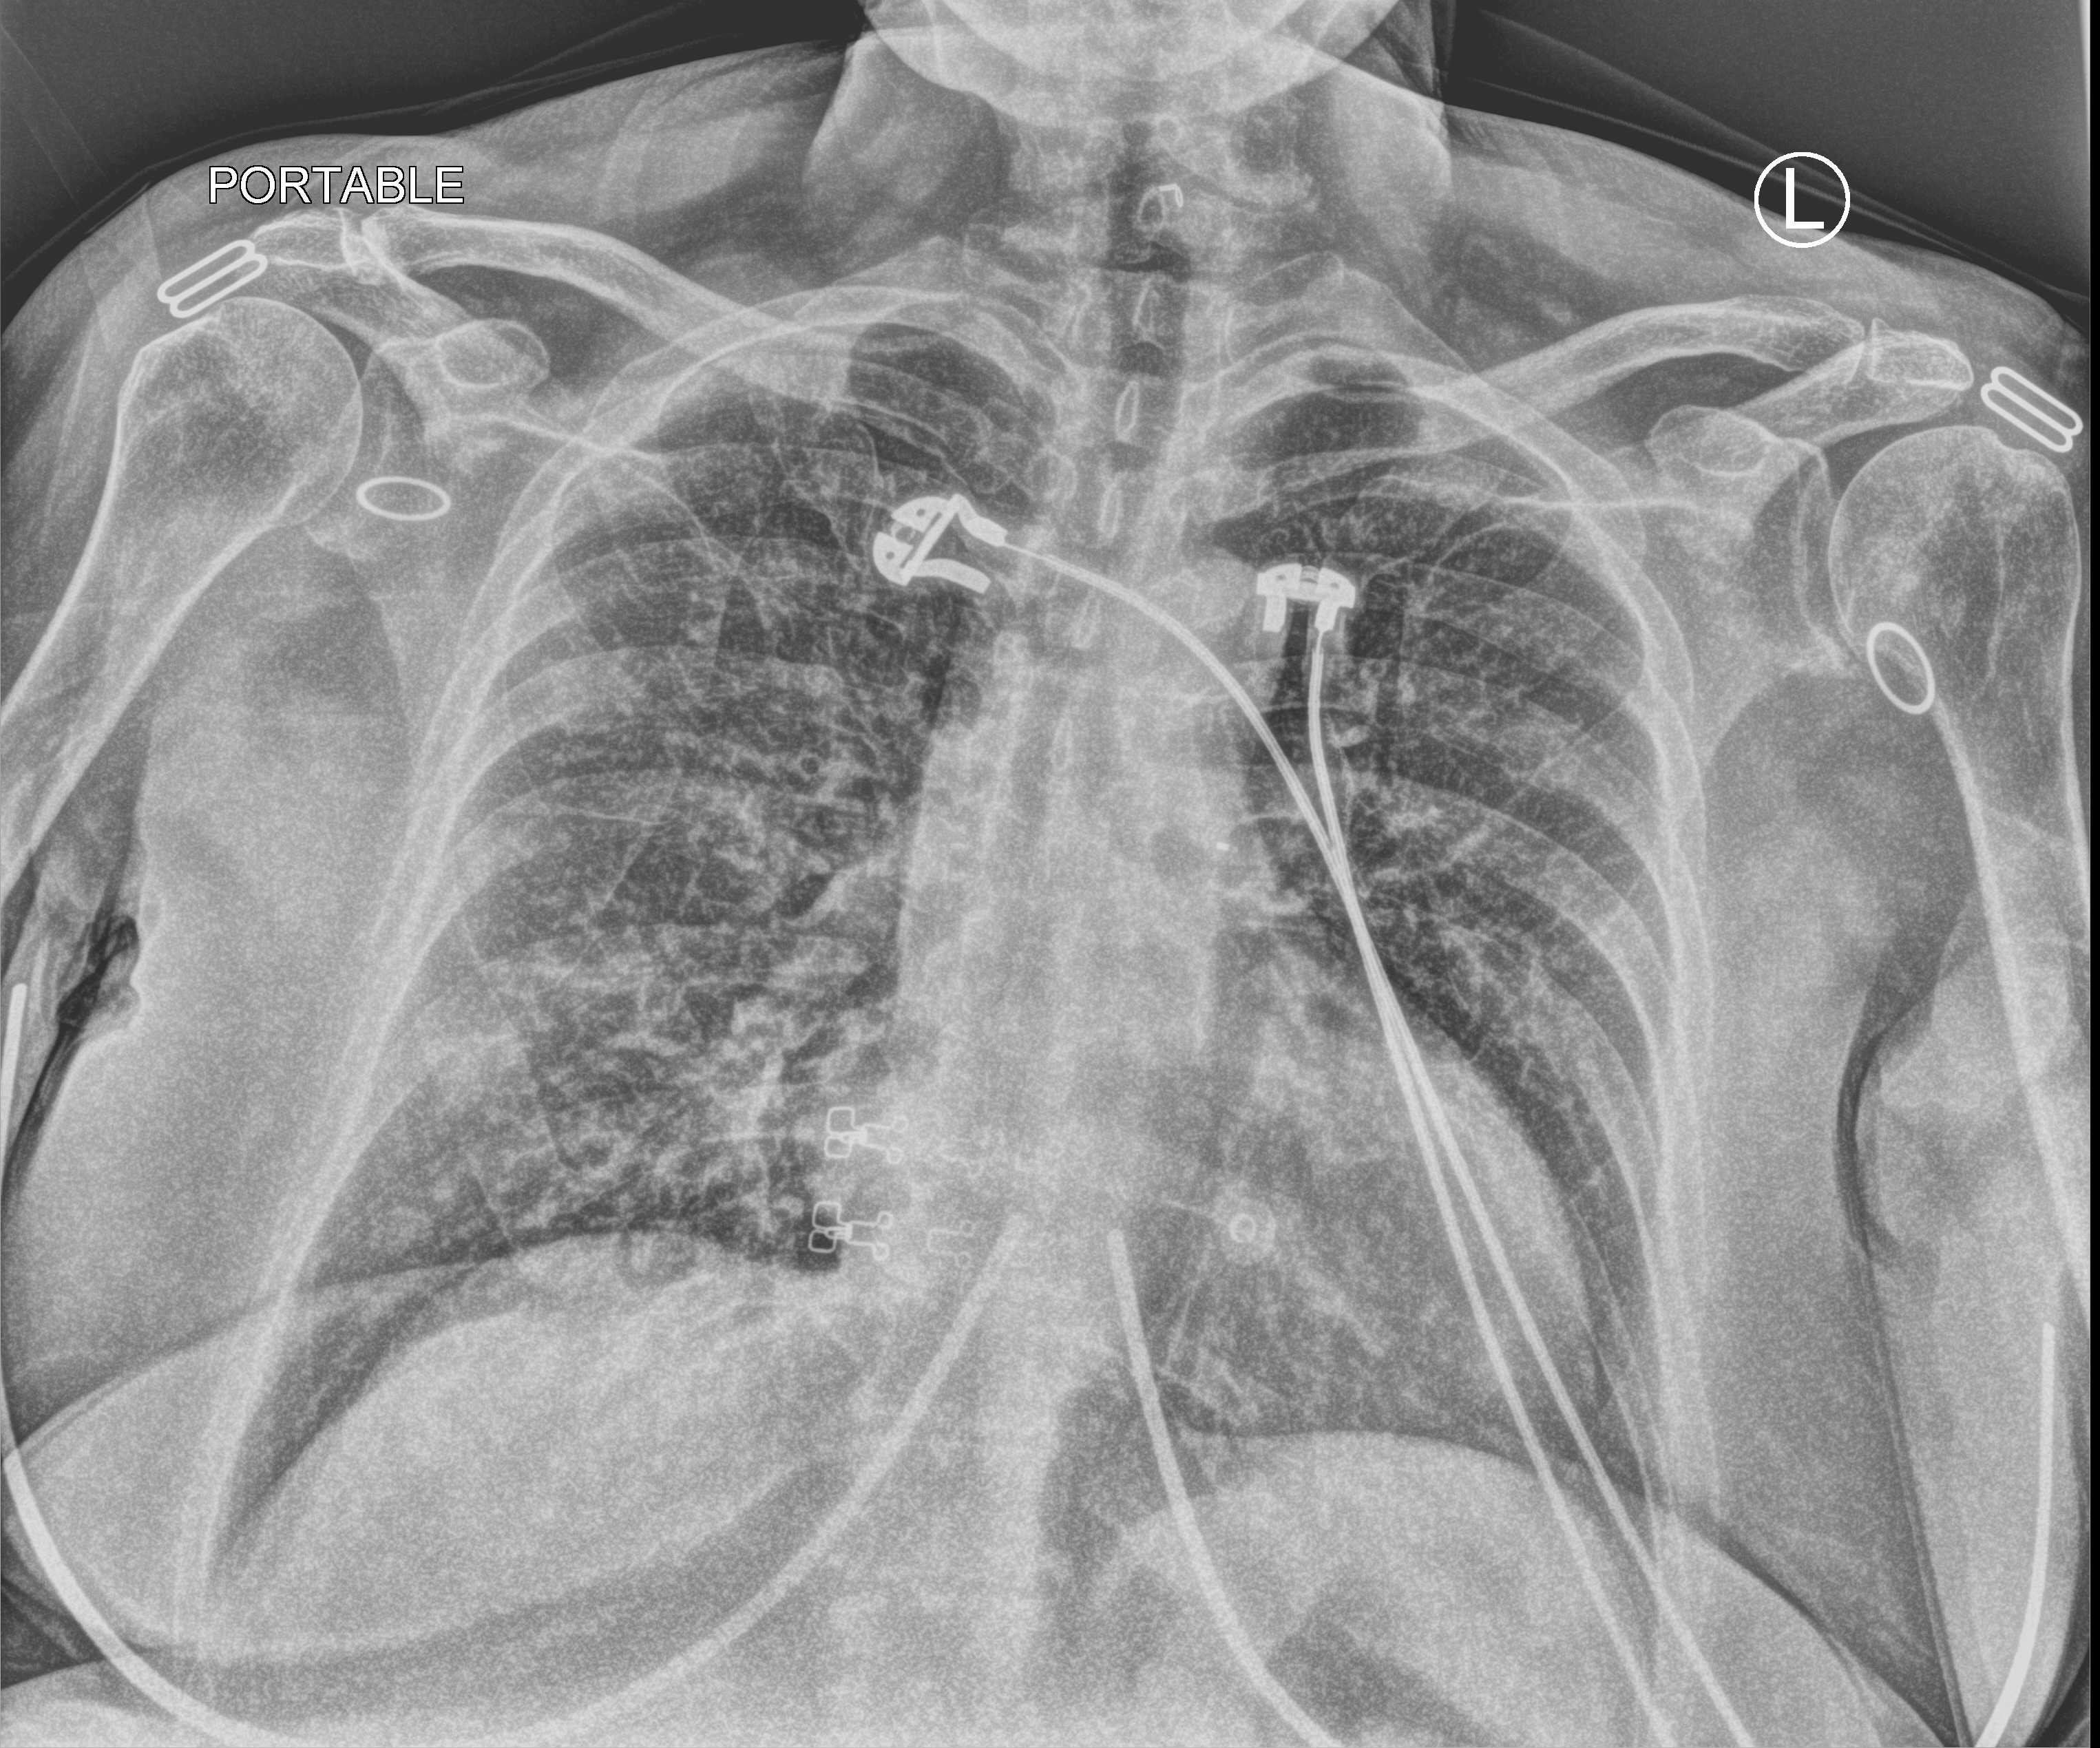
Portable chest radiograph. Female patient hospitalised with COVID-19, age 60–74 years.
From the hospital-stay record, not from the radiograph (when in the stay this image was taken is not recorded): mechanically ventilated during this hospital stay: no.